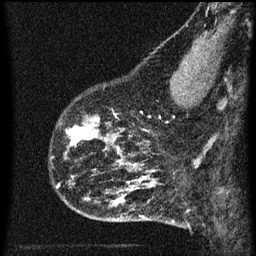
Breast MRI (dynamic contrast-enhanced), one sagittal slice. Position 16 of 60 along the scan axis. Dynamic contrast-enhanced series, image 2 of 3 at this slice position (ordered by acquisition). 1.5 T. TE 4.2 ms, TR 8 ms. 2 mm slice thickness. 256 × 256 image matrix, field of view 180 × 180 mm. Patient: female, 43 years.
Annotated regions visible in this slice (semi-automatically segmented with operator editing):
- analysis volume of interest (the breast-tissue region the enhancement analysis was run in; not a lesion): bounding box <56,108,104,153> (left, top, right, bottom; pixels)
- tumour enhancement mask (voxels above the 70 % enhancement threshold inside the analysis volume of interest): <66,116,103,147>